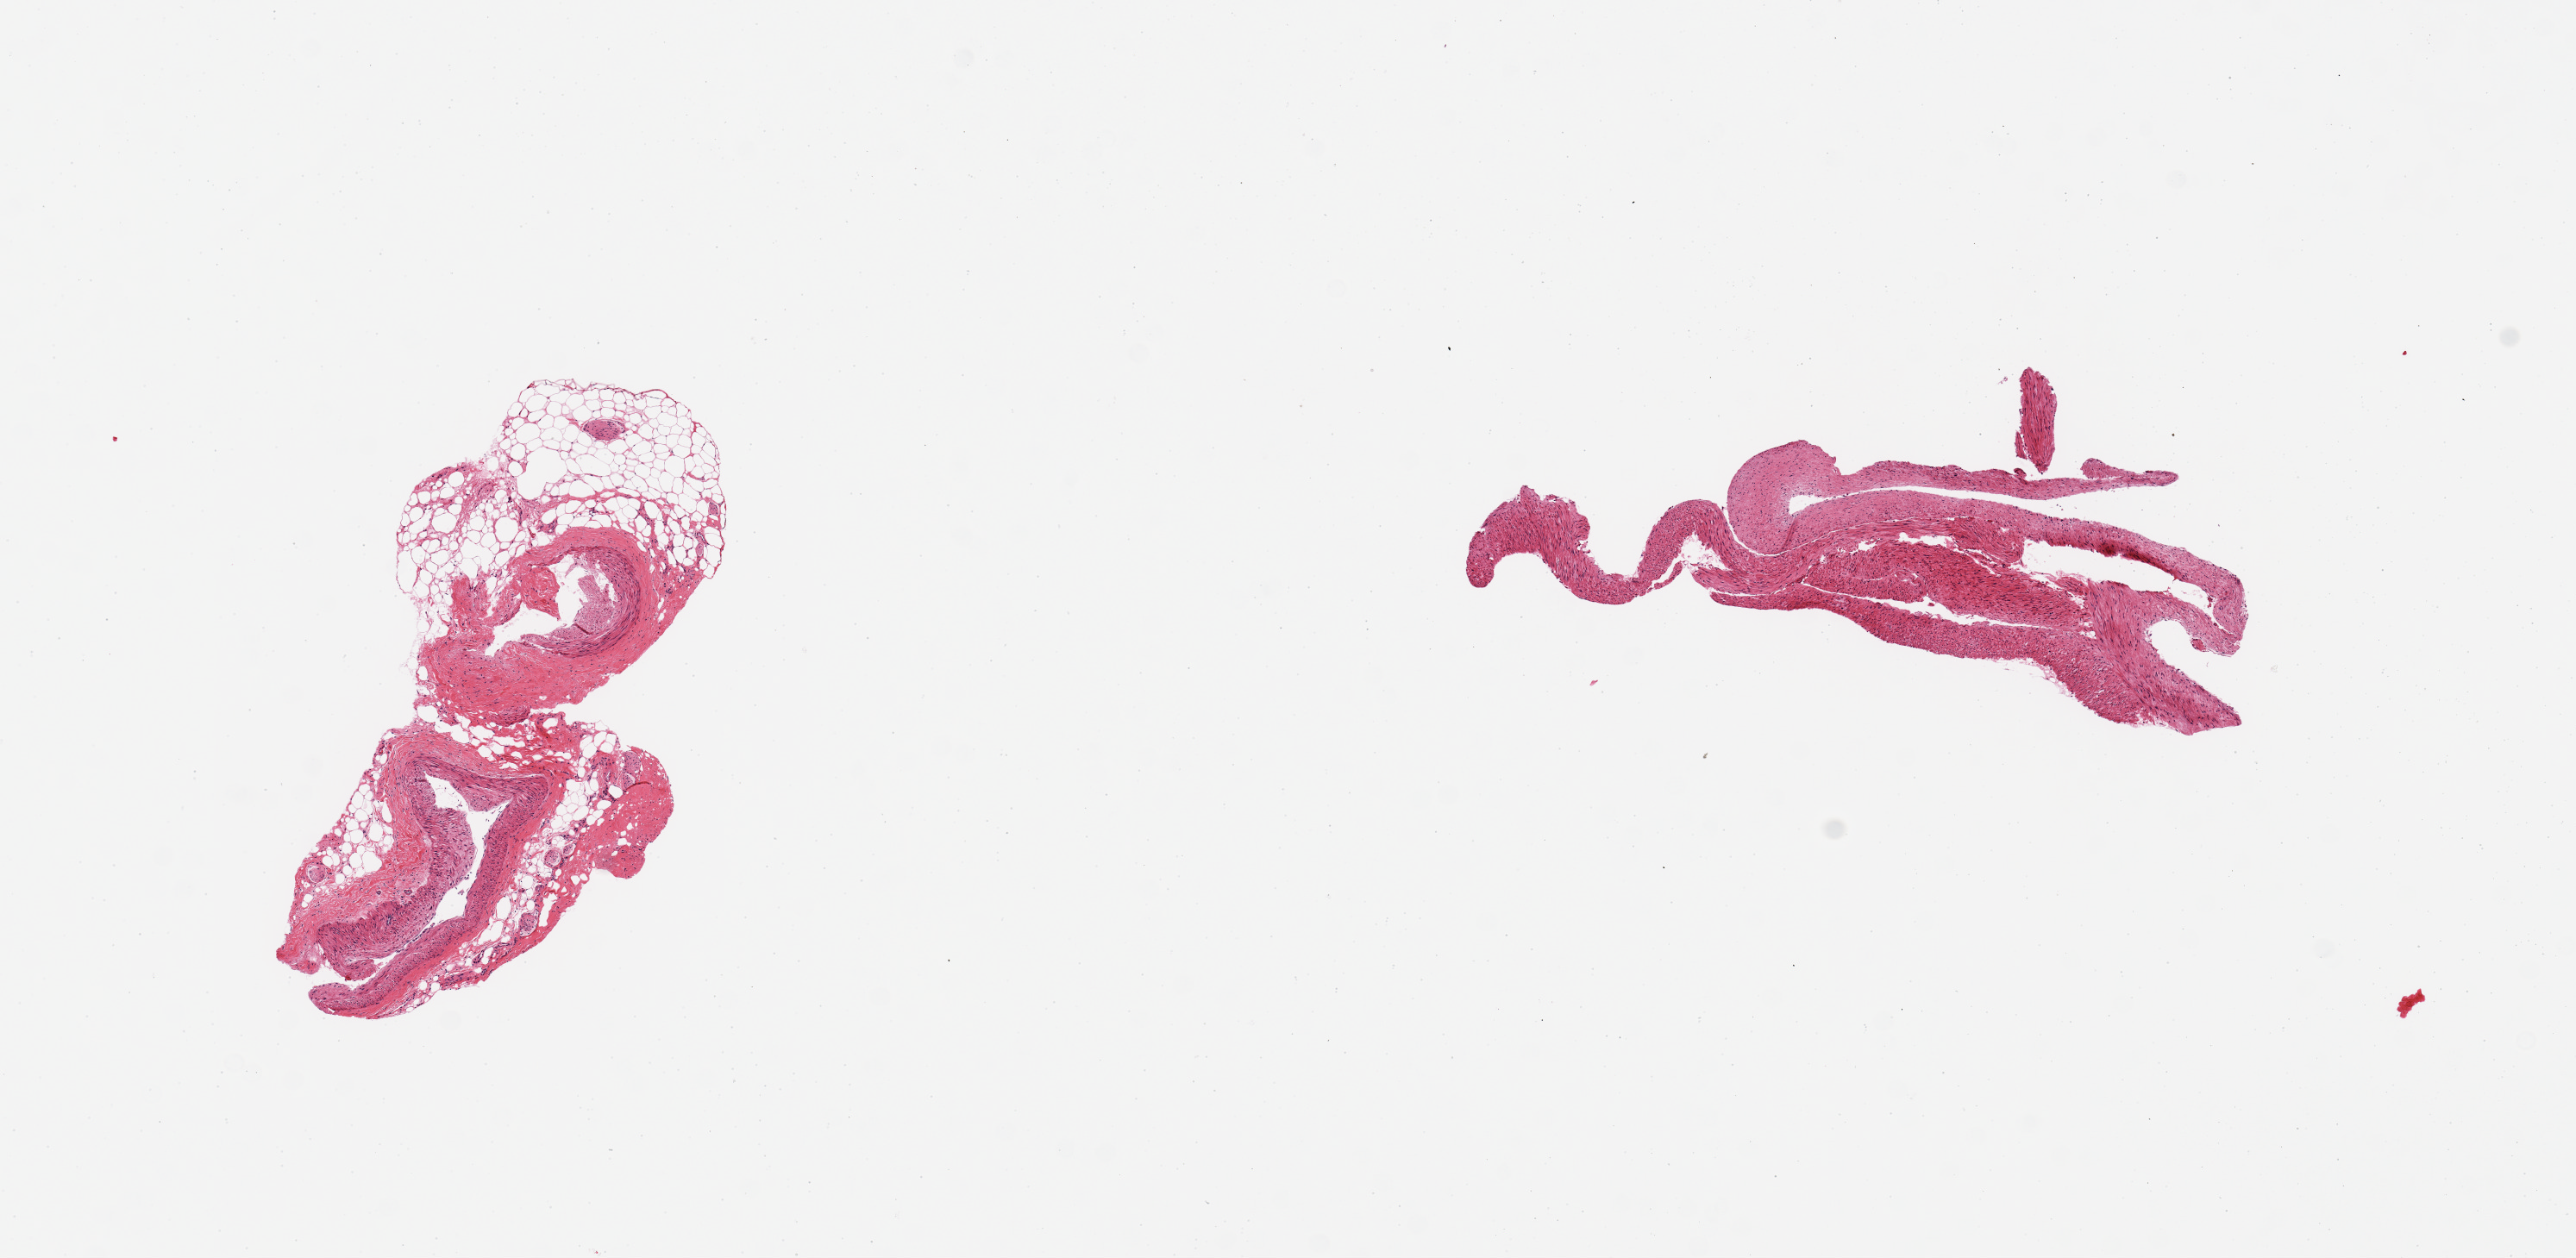
Digitized haematoxylin and eosin-stained section — shown as a low-resolution overview of the whole scanned area (about 11.8 x 5.8 mm), PAXgene-fixed, paraffin-embedded tissue, section of coronary artery (target tissue), tissue donor sample. Female donor.
• review note (as recorded): 2 pieces, fragmented, aderhent fat up to ~0.6mm on one. No signifianct atherosis noted